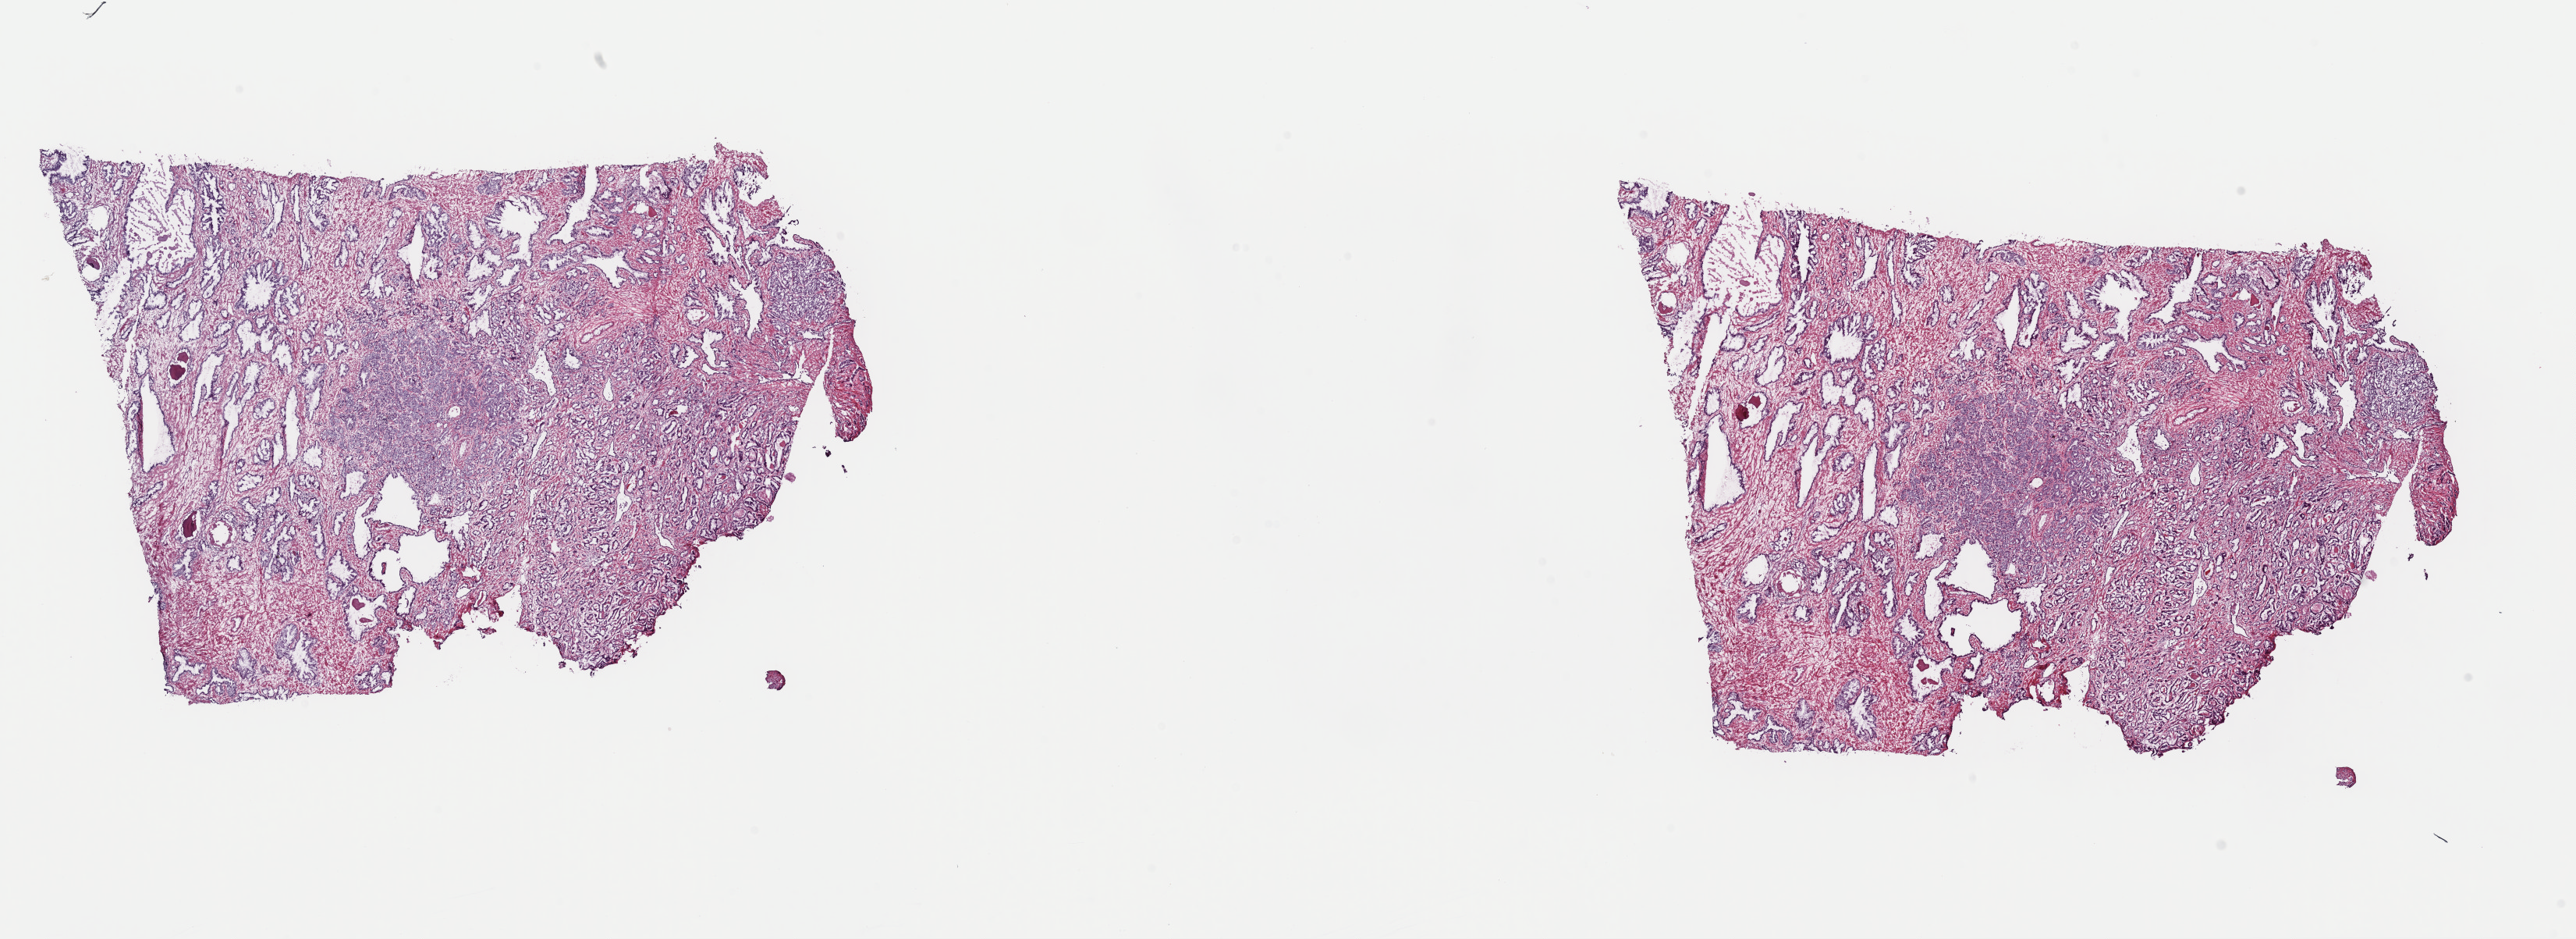
H&E-stained whole-slide image, a low-resolution overview of the entire scanned area, about 26.1 x 9.5 mm. Frozen section from the top of the tissue portion. Prostate, primary tumour sample. Patient: male, age at initial diagnosis 65 years. Gleason score: 6 (3+3). Pathologist review of this section (percent, as recorded): tumour cells 65%, tumour nuclei 65%, normal cells 35%, stromal cells 0%, necrosis 0%. Infiltration values recorded for this section: lymphocyte infiltration 0%, monocyte infiltration 0%, neutrophil infiltration 0%.
Pathologic diagnosis: Adenocarcinoma, NOS (prostate gland). Lymph nodes positive (case pathology): 0 of 30 examined.